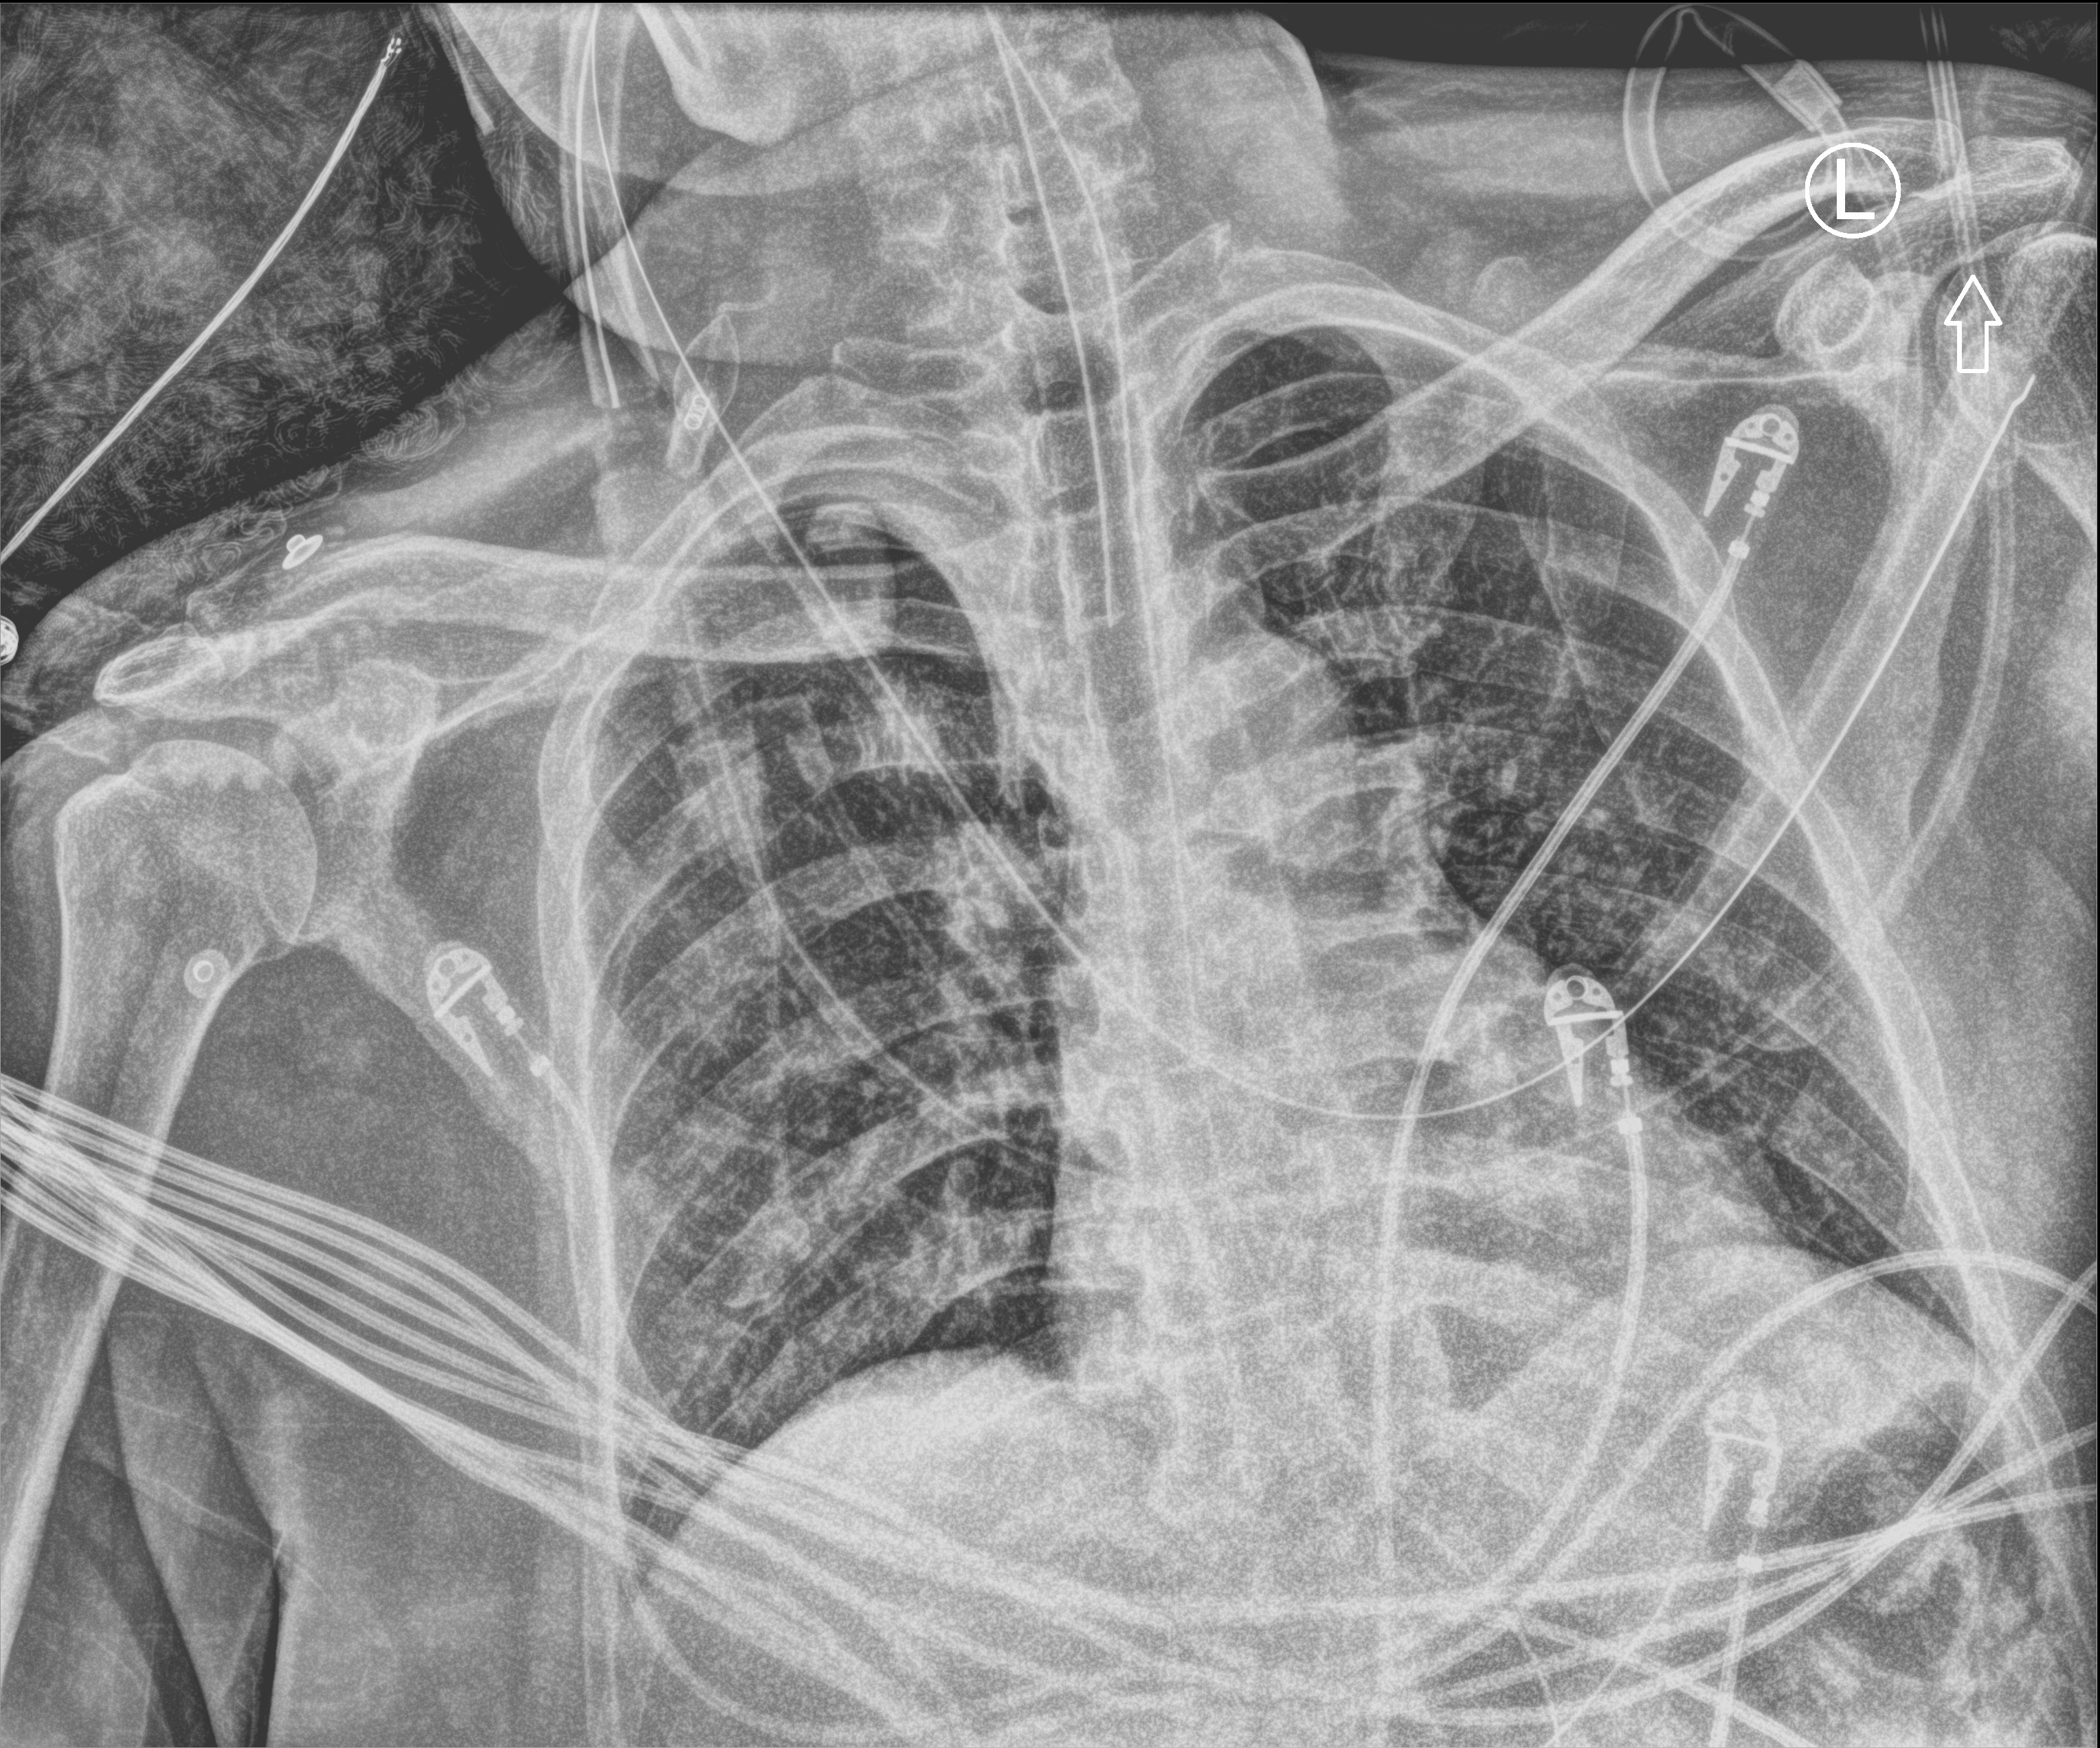
Portable chest radiograph; anteroposterior (AP) projection. Patient hospitalised with COVID-19, aged 18–59 years.
Hospital-stay facts (about this admission, not read from this image; timing relative to this image not recorded):
- mechanically ventilated during this hospital stay: yes
- length of hospital stay: 37 days
- COPD (admission record): no